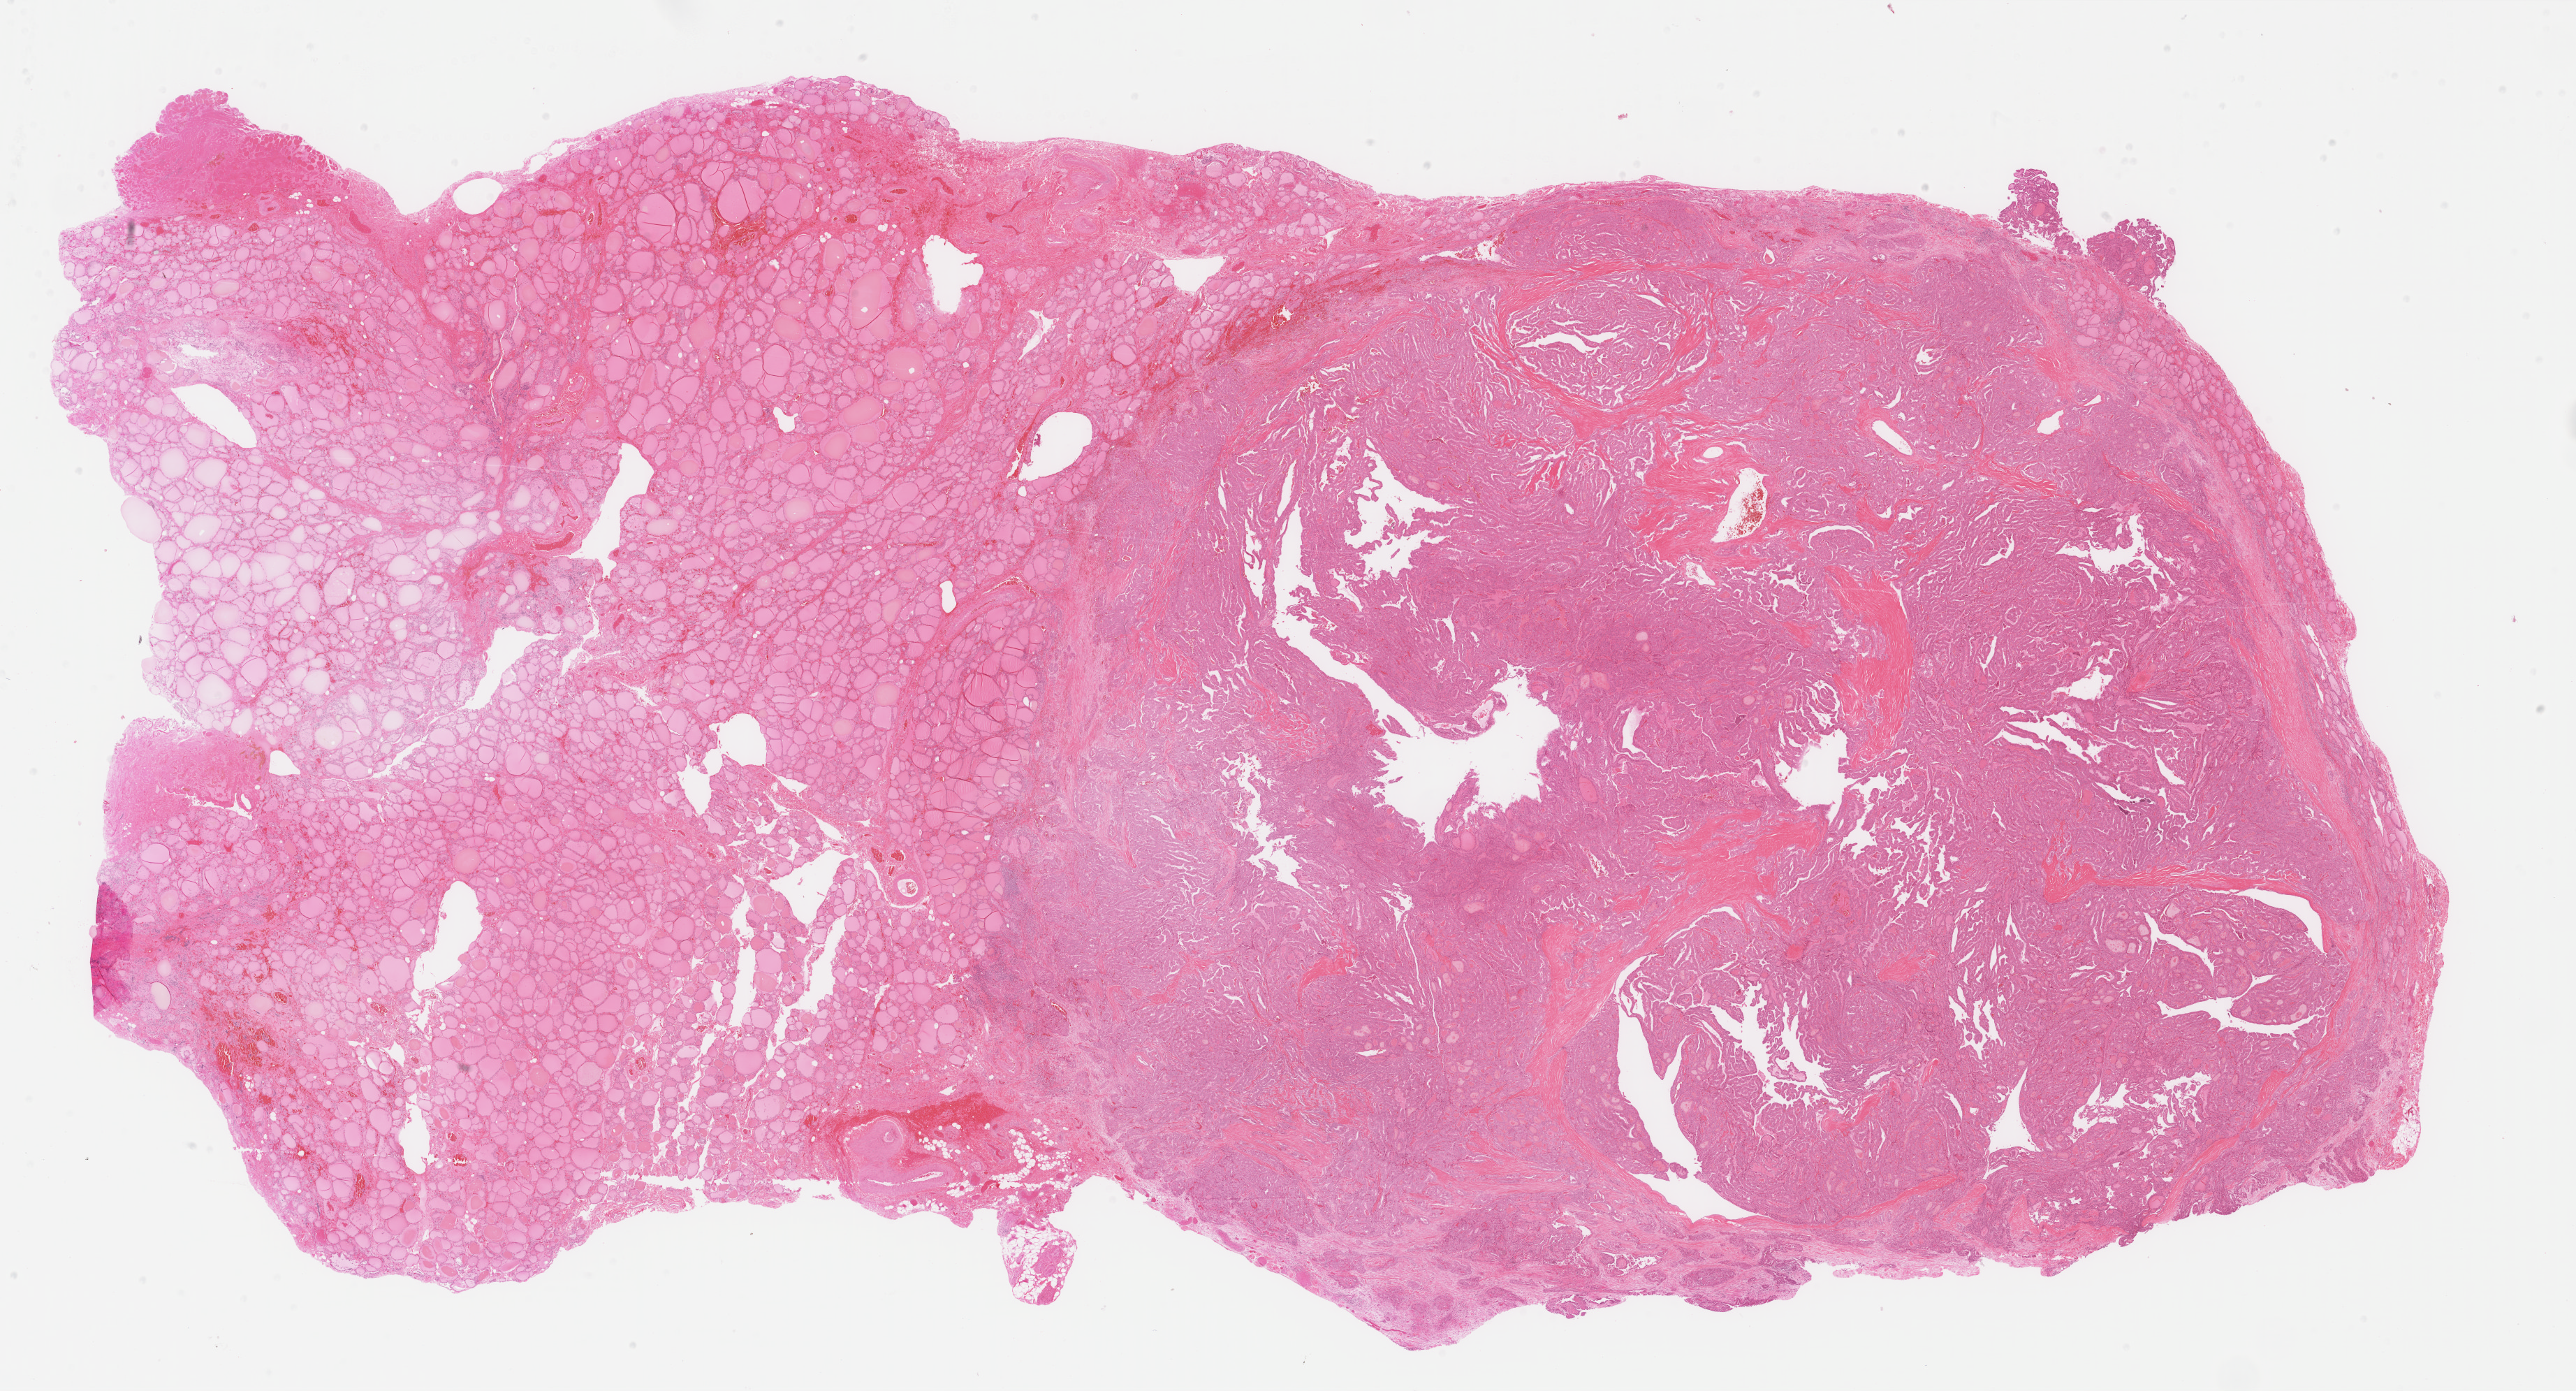
Hematoxylin and eosin (H&E) stained whole-slide image — shown as a low-resolution overview of the whole scanned area (about 29.3 x 15.8 mm, slide scanned at 40x), formalin-fixed paraffin-embedded (FFPE) diagnostic section, thyroid, primary tumour sample. Female, age 44 years at initial diagnosis.
* TNM: T3 N1b M0
* pathologic diagnosis: Papillary adenocarcinoma, NOS (thyroid gland)
* lymph nodes positive (case pathology): 15 of 30 examined
* AJCC pathologic stage: I